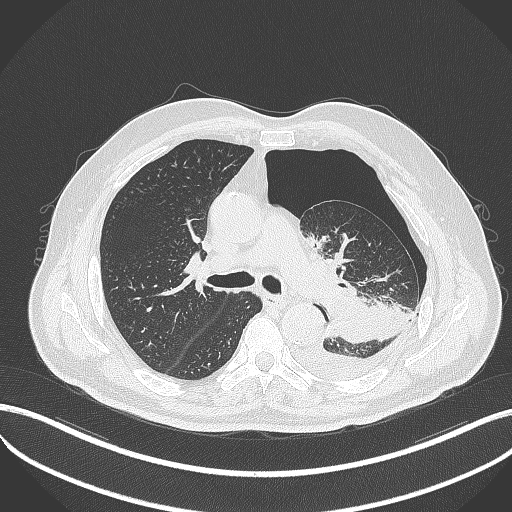
Chest CT, one axial slice; slice 324 of 464 in the series (ordered by position); reconstruction kernel B70f; 120 kVp; lung window (W 1500 / L -600 HU); 1 mm slice thickness; 512 × 512 image matrix, field of view 400 × 400 mm. Patient: male, 76 years. From the clinical record (not read from this slice): clinical TNM (as recorded): T3 N0 M1b.
Structures marked on this image (bounding box drawn by a radiologist):
- lung tumour (recorded histology: adenocarcinoma): bounding box (x1, y1, x2, y2) in pixels: (324, 286, 397, 344)